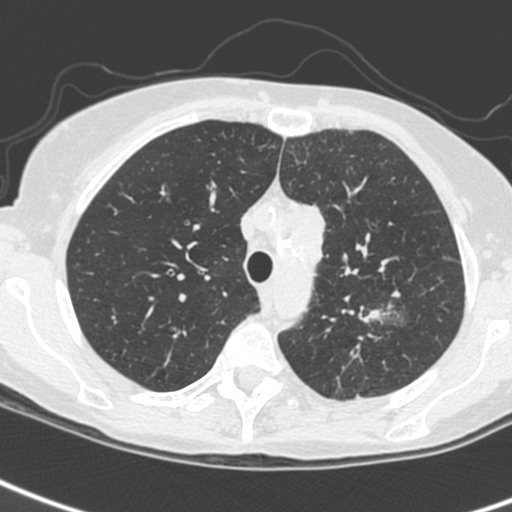
Low-dose screening chest CT, axial slice, baseline screening round, lung window (W 1500 / L -600 HU), slice 53 of 242 in the series, 512 × 512 image matrix. Female participant, aged 61 years at enrolment. Current smoker at enrolment.
• Expert-annotated lung lesion, bounding box (x1, y1, x2, y2) in pixels: (343, 290, 411, 347).
• The screening reader recorded 2 non-calcified nodules or masses ≥4 mm on this exam (left upper lobe, left upper lobe); which of them this box marks is not recorded.
• Official screen result: positive, change unspecified: nodule(s) >= 4 mm or enlarging nodule(s), mass(es), or other non-specific abnormalities suspicious for lung cancer.
• Participant outcome: lung cancer diagnosed 29 days after this screen — small cell carcinoma, NOS, left upper lobe, stage IV (AJCC 6th edition).